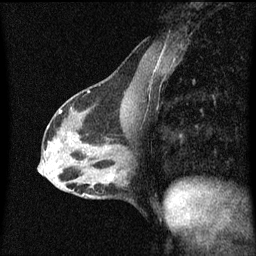
Breast MRI (dynamic contrast-enhanced), one sagittal slice. Slice 29 of 60 in the series (ordered by position). Dynamic contrast-enhanced series, image 2 of 3 at this slice position (ordered by acquisition). 1.5 T. TE 4.2 ms, TR 8.4 ms. 2 mm slice thickness. 256 × 256 image matrix, field of view 200 × 200 mm. Patient: female, 40 years.
Structures marked on this image (semi-automatic segmentation, software-assisted and operator-edited):
- analysis volume of interest (the breast-tissue region the enhancement analysis was run in; not a lesion): bounding box <78,166,120,199> (left, top, right, bottom; pixels)
- tumour enhancement mask (voxels above the 70 % enhancement threshold inside the analysis volume of interest): <84,176,114,197>